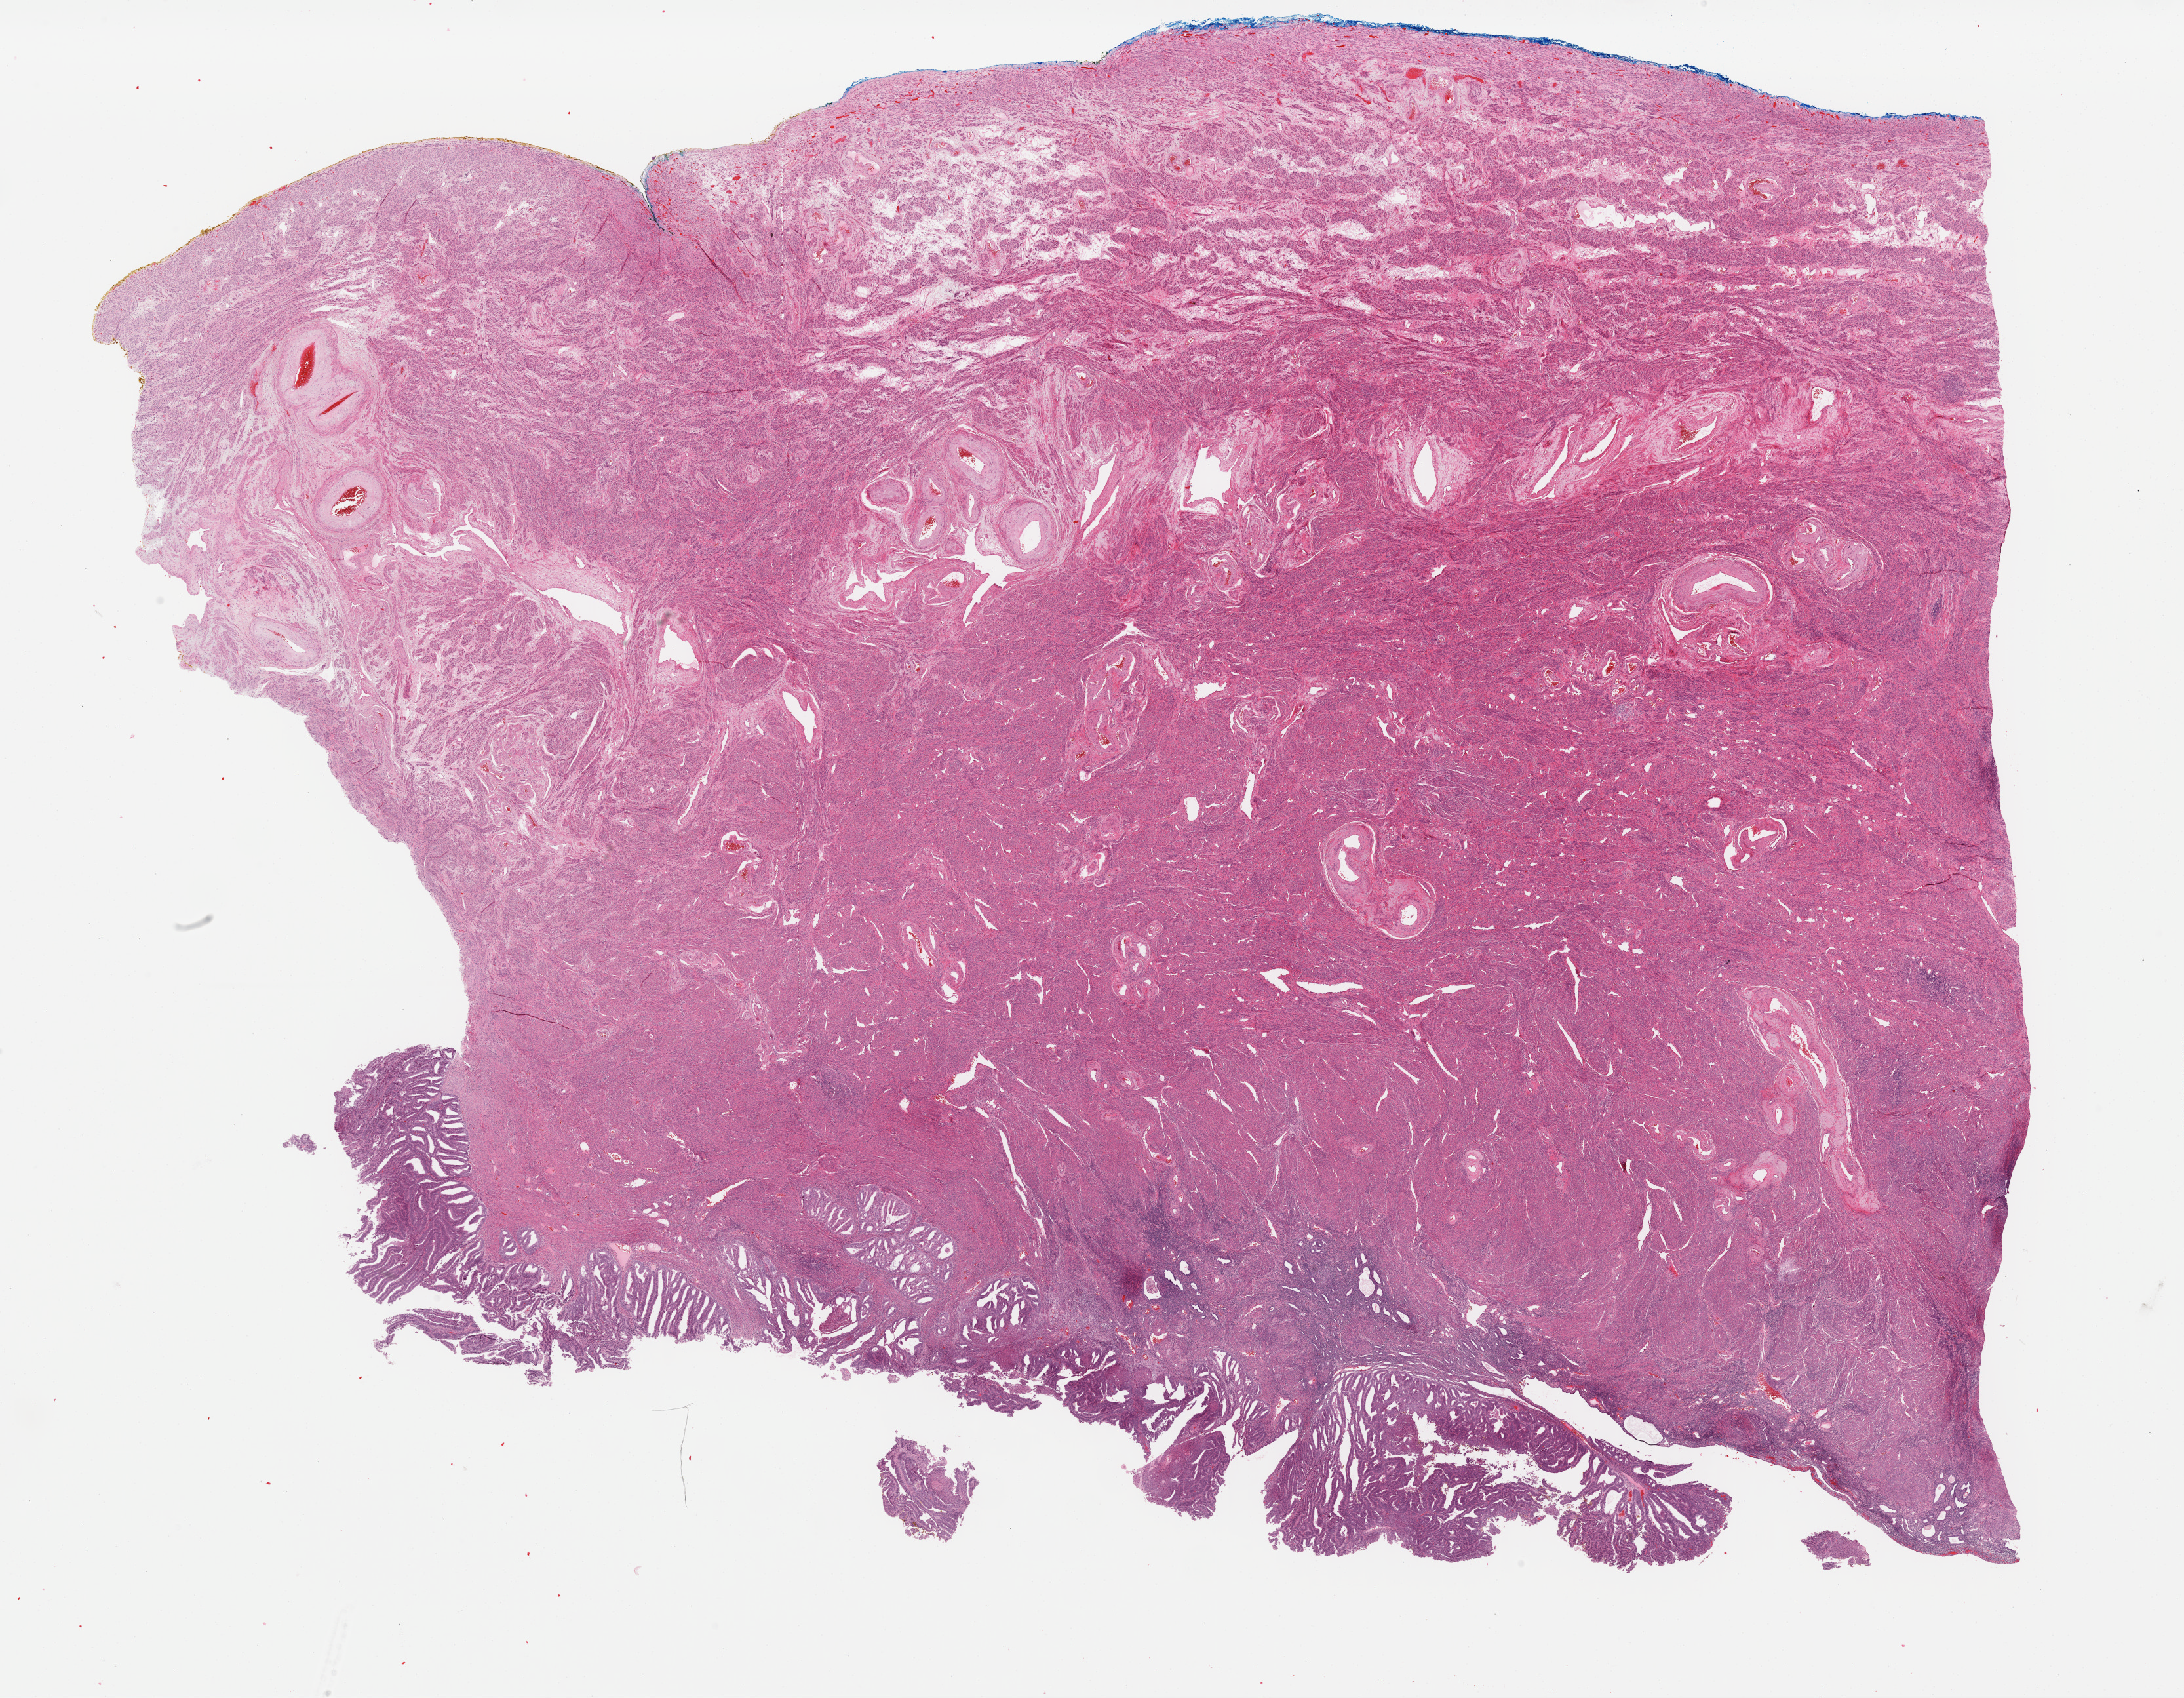
Digitized H&E-stained tissue section (whole slide) — shown as a low-resolution overview of the whole scanned area (about 26.3 x 20.5 mm); FFPE section; primary tumour sample from the uterus. Female, age 82 years at initial diagnosis. Histologic grade: G1 (well differentiated).
FIGO stage: IB. Diagnosis: Endometrioid adenocarcinoma, NOS (endometrium).